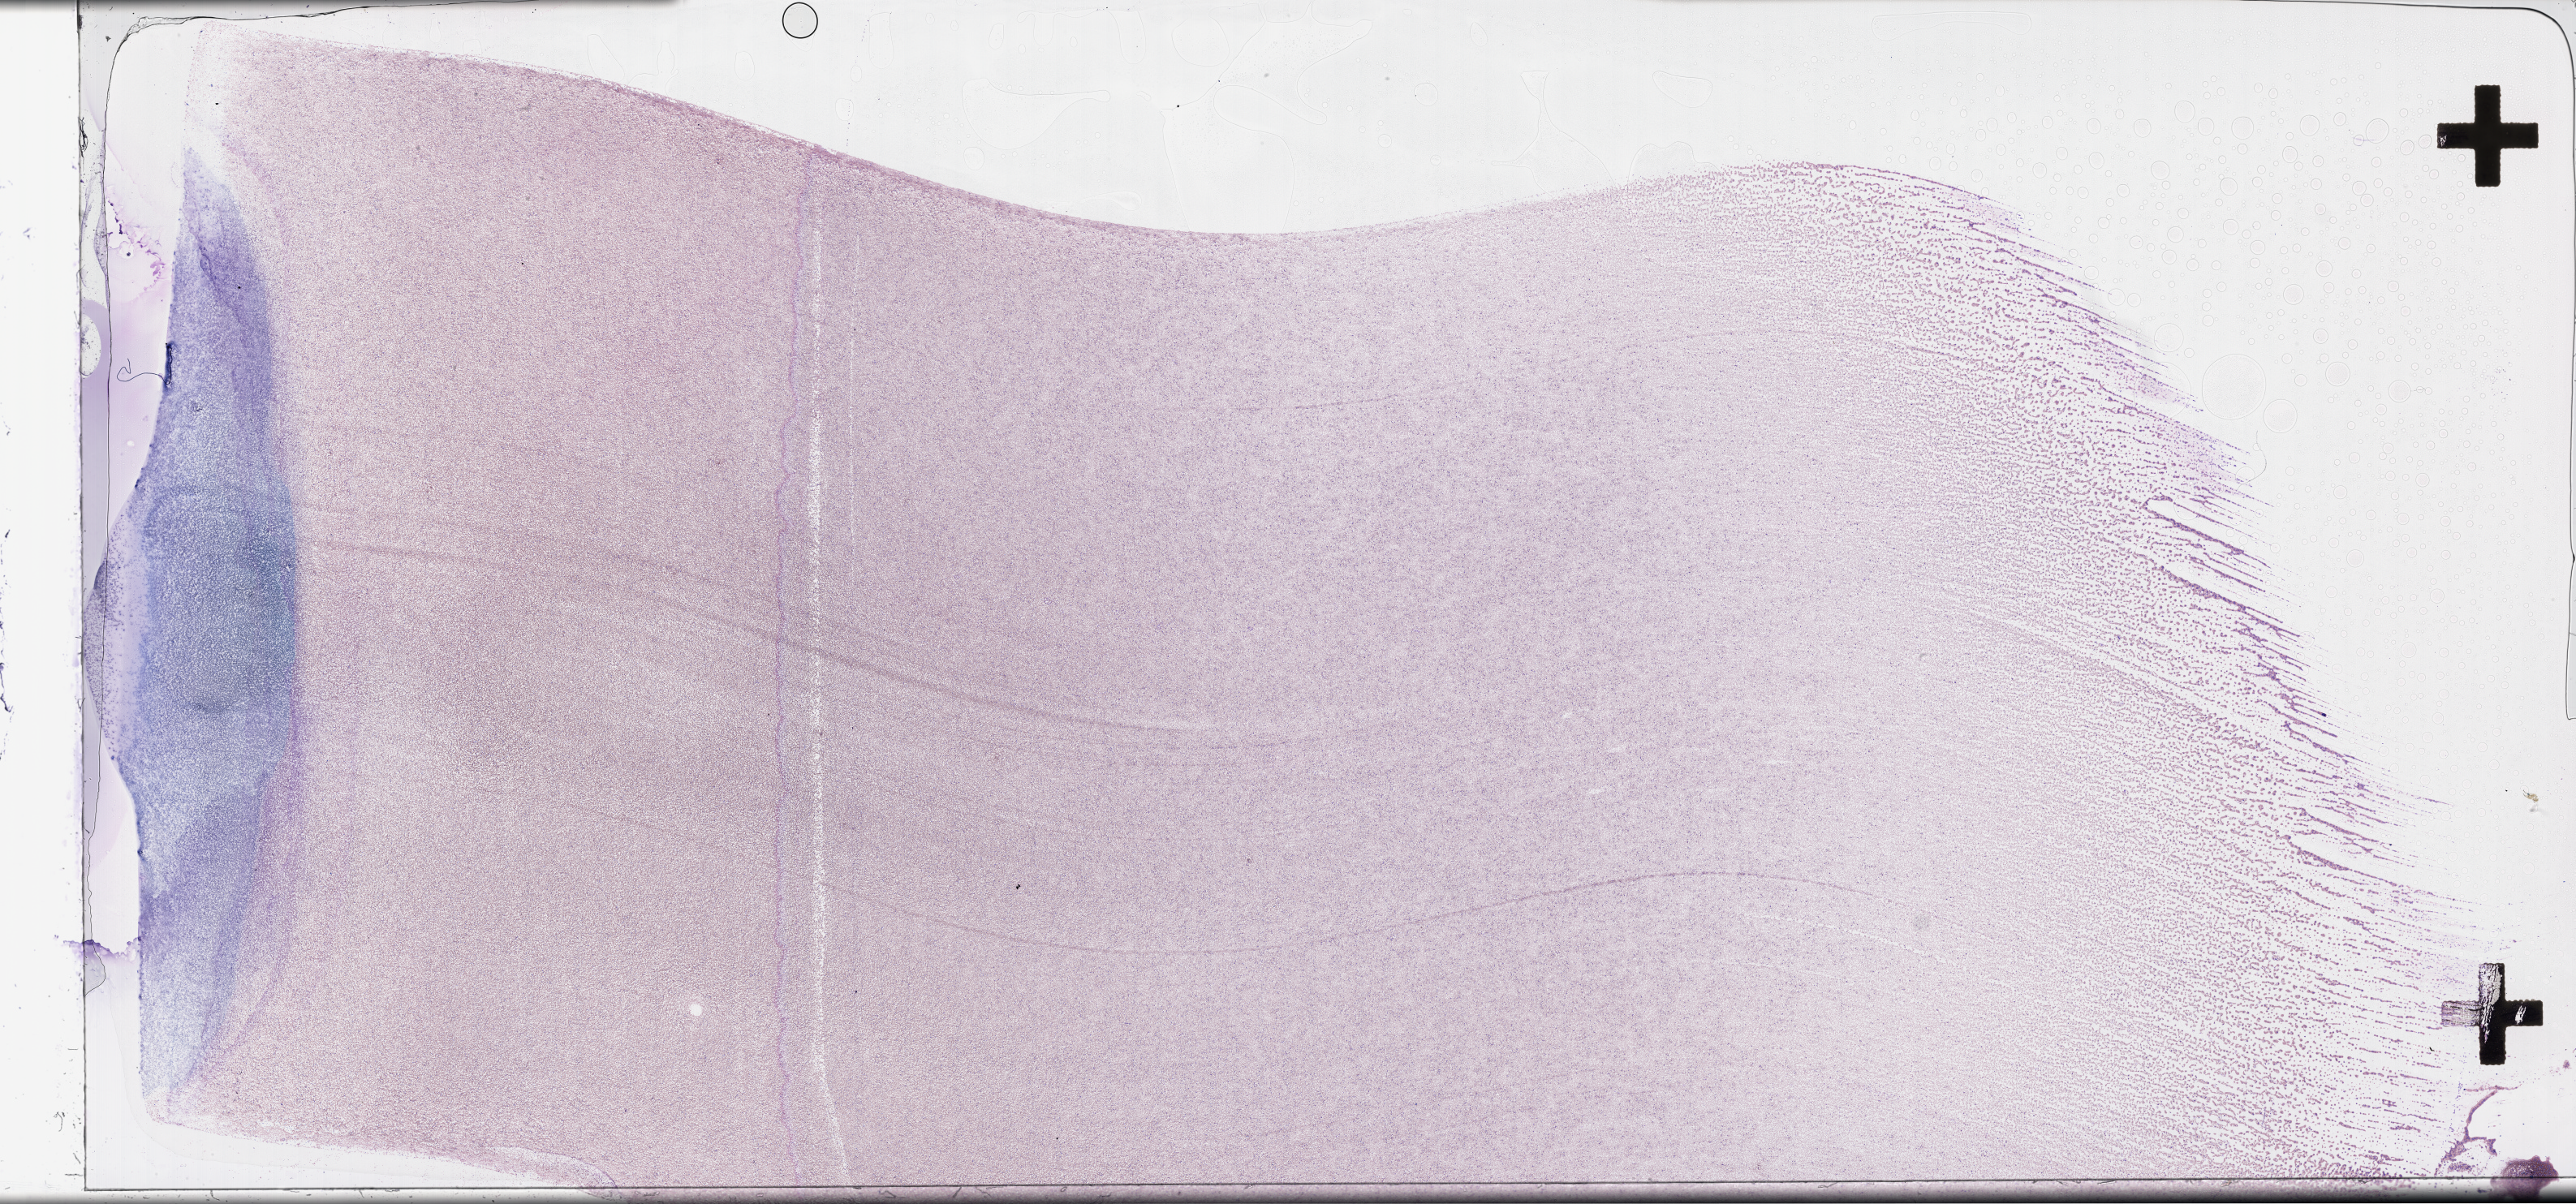
Whole-slide histology image, Hematoxylin and eosin (H&E) stained, a low-resolution overview of the entire scanned area, about 51.3 x 24.0 mm, peripheral blood (leukaemic) sample. Male, 63 y/o.
* FAB classification: M1
* WHO classification: AML with mutated NPM1
* diagnosis: Acute Myeloid Leukemia